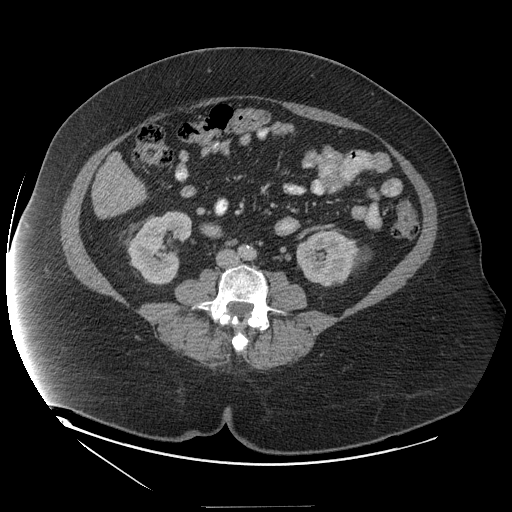
Contrast-enhanced abdominal CT (liver protocol), one axial slice. Slice 26 of 127 in the series (ordered by position). Reconstruction kernel STANDARD. 140 kVp. Soft-tissue window (W 400 / L 40 HU). 512 × 512 image matrix. Case-level facts recorded for this patient, not image findings: diagnosis: hepatocellular carcinoma (patient treated with transarterial chemoembolisation; whether this scan precedes or follows treatment is not stated here); TNM stage (as recorded): Stage-II; Child-Pugh class: A; tumour differentiation: well differentiated; tumour nodularity: multinodular.
Annotated regions visible in this slice (semi-automatic segmentation, software-assisted and operator-edited):
- liver parenchyma outside the tumour (the mass and vessels are separate outlines, so this box may not span the whole liver): bounding box <92,156,136,218> (left, top, right, bottom; pixels)